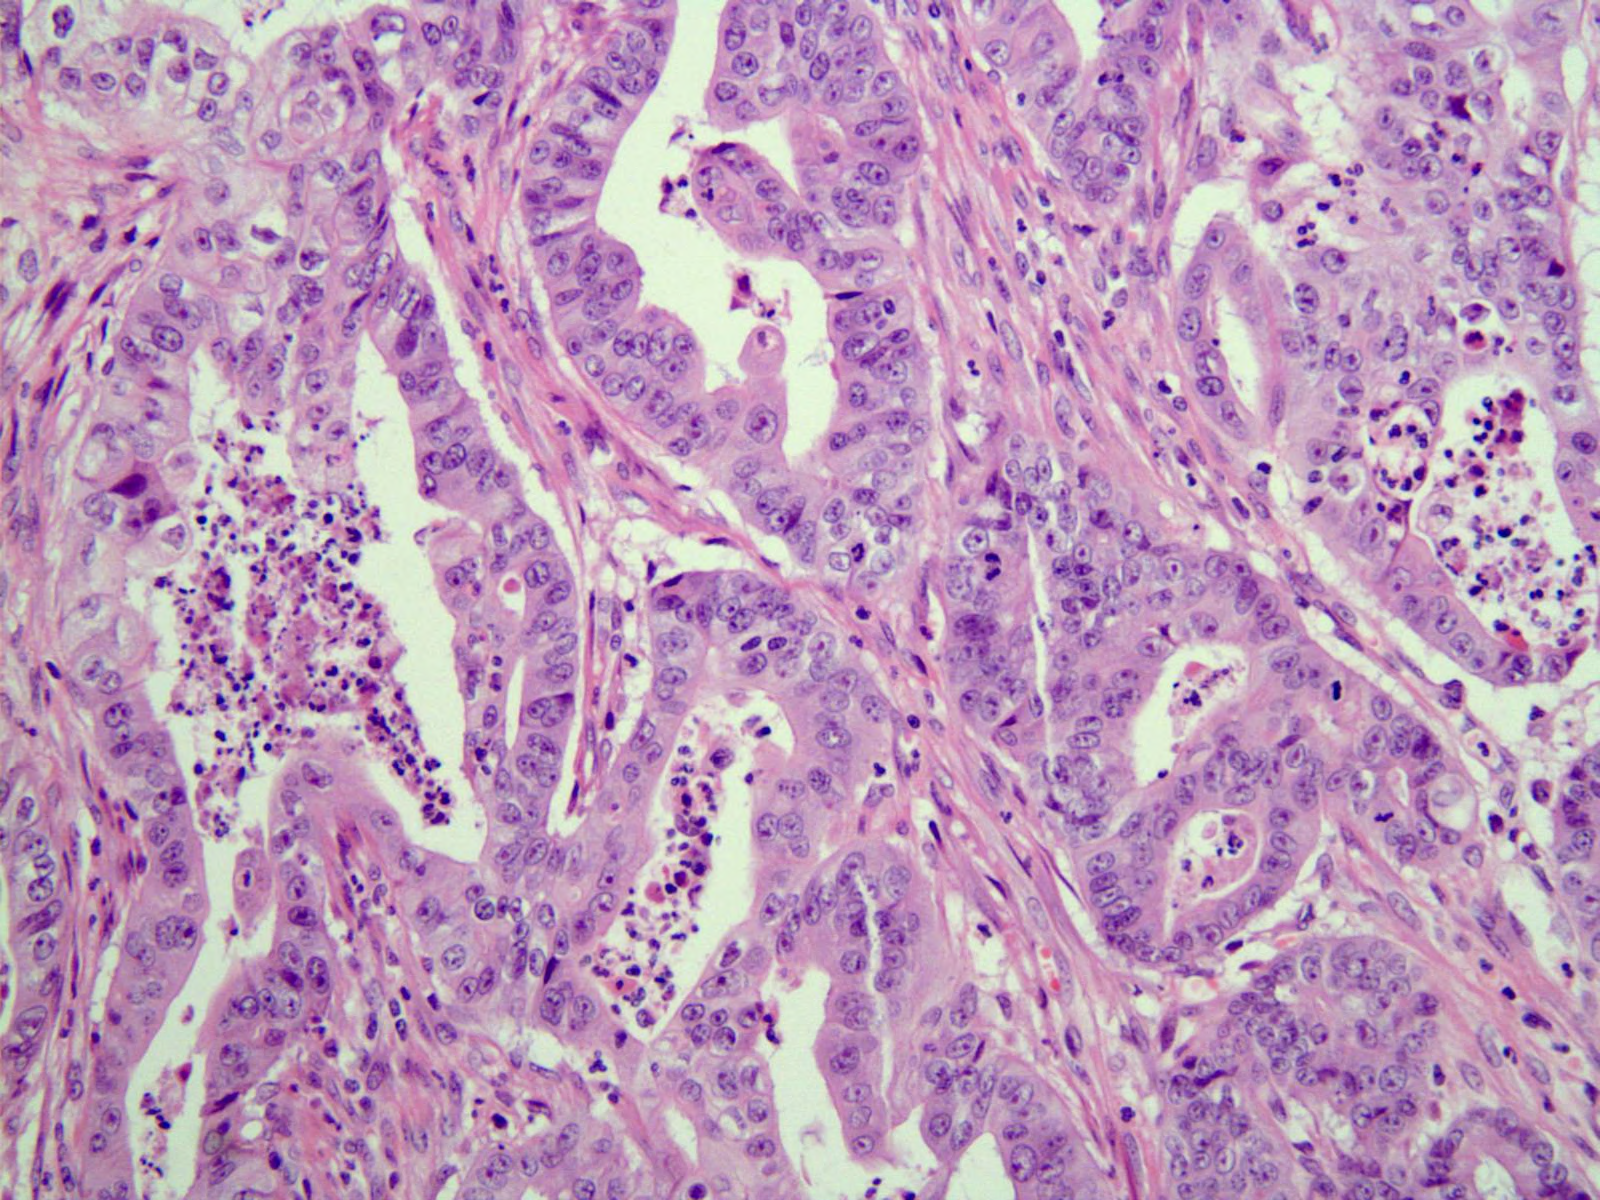
Hematoxylin and eosin (H&E) stained micrograph of a single small tissue field, about 0.8 x 0.6 mm across, FFPE section, primary tumour sample from the stomach. Female, age 66 years at initial diagnosis. Histologic grade: G1 (well differentiated).
Diagnosis: Adenocarcinoma, NOS (cardia, NOS).